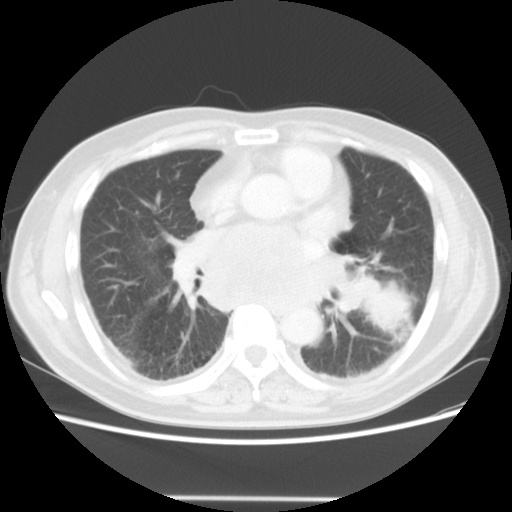
Chest CT, one axial slice; position 25 of 56 along the scan axis; reconstruction kernel STANDARD; 140 kVp; lung window (W 1500 / L -600 HU); 5 mm slice thickness; 512 × 512 image matrix. Patient: male, 66 years. Case-level facts recorded for this patient, not image findings: clinical TNM (as recorded): T4 N3 M0; histopathological grade: G3.
Outlined on this slice (bounding box drawn by a radiologist):
- lung tumour (recorded histology: small cell carcinoma): bounding box [x1, y1, x2, y2] px = [343, 271, 419, 339]